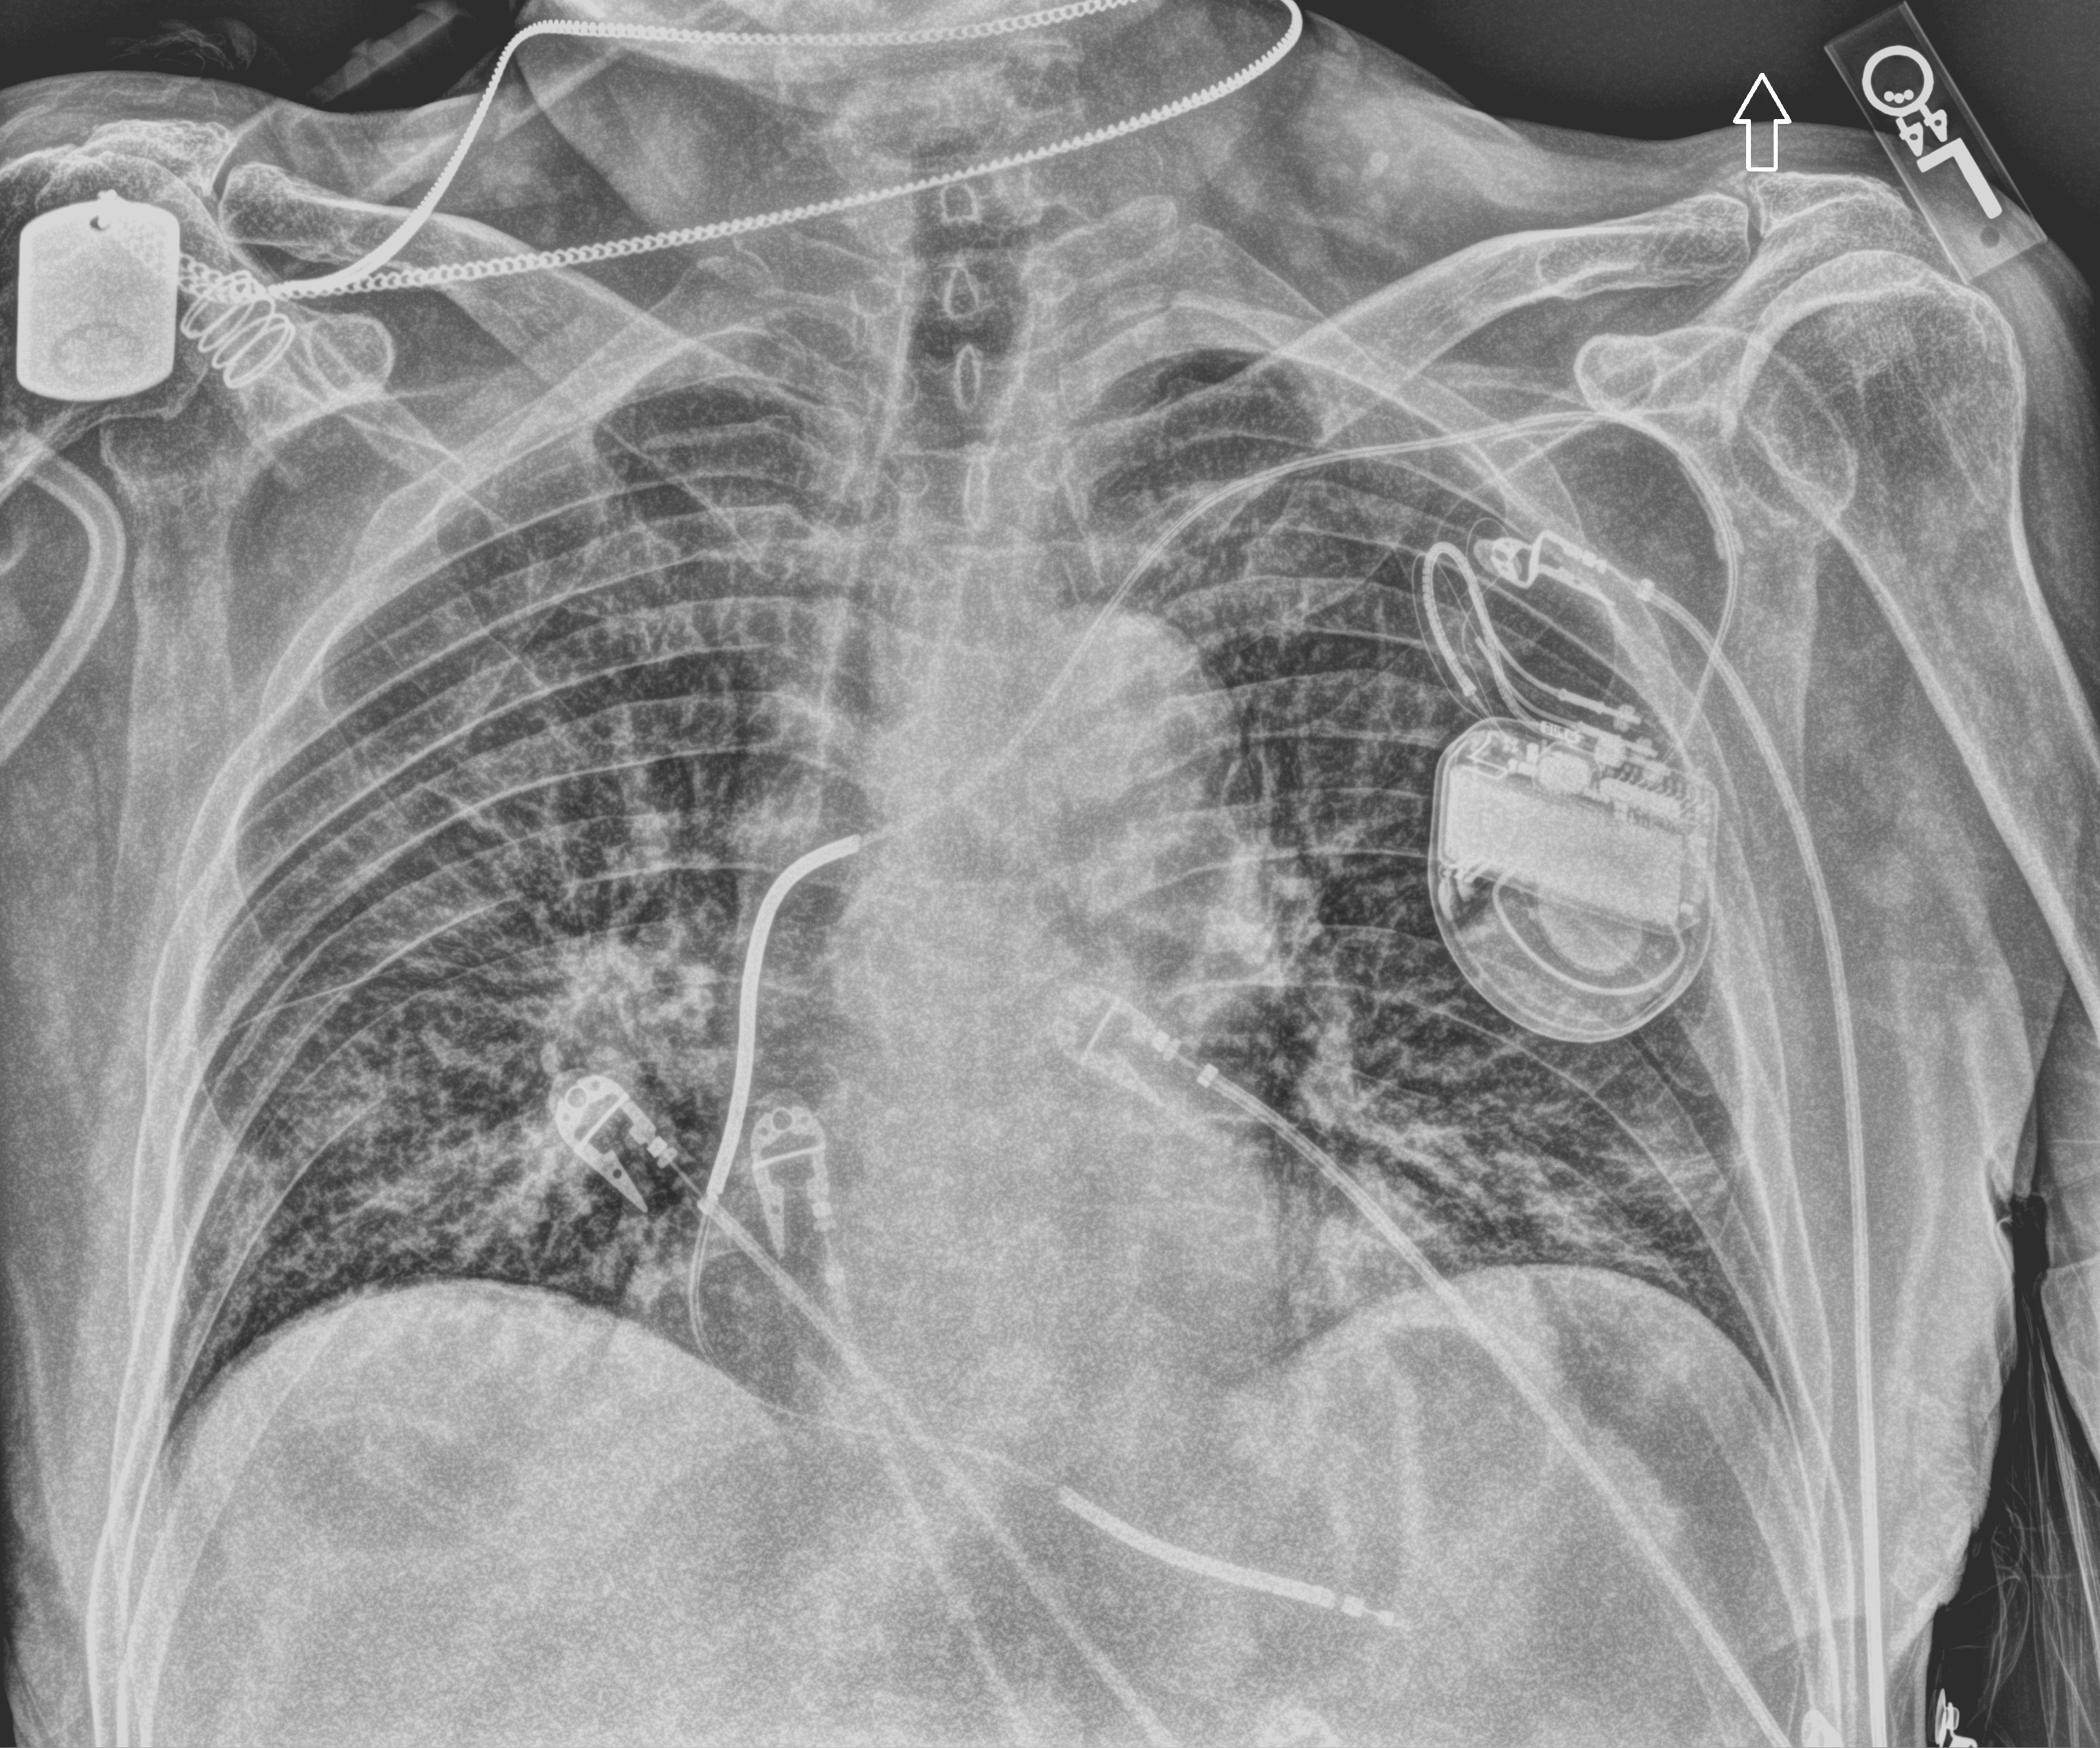
Bedside chest radiograph (computed radiography); anteroposterior (AP) projection. Male patient hospitalised with COVID-19, age 75–90 years.
Hospital-stay facts (about this admission, not read from this image; timing relative to this image not recorded): admitted to intensive care during this hospital stay: no.